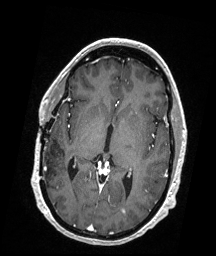
Brain MRI from a brain-tumour surgery series, one axial slice. Slice 95 of 176 in the series (ordered by position). T1-weighted post-contrast. 216 × 256 image matrix, field of view 211 × 250 mm. Case-level facts recorded for this patient, not image findings: histopathology: Demyelinating Lesions (Multiple Sclerosis Plaques); tumour location: Left Occipital.
Annotated regions visible in this slice (expert manual segmentation):
- tumour: bounding box (x1, y1, x2, y2) in pixels: (120, 208, 127, 215)